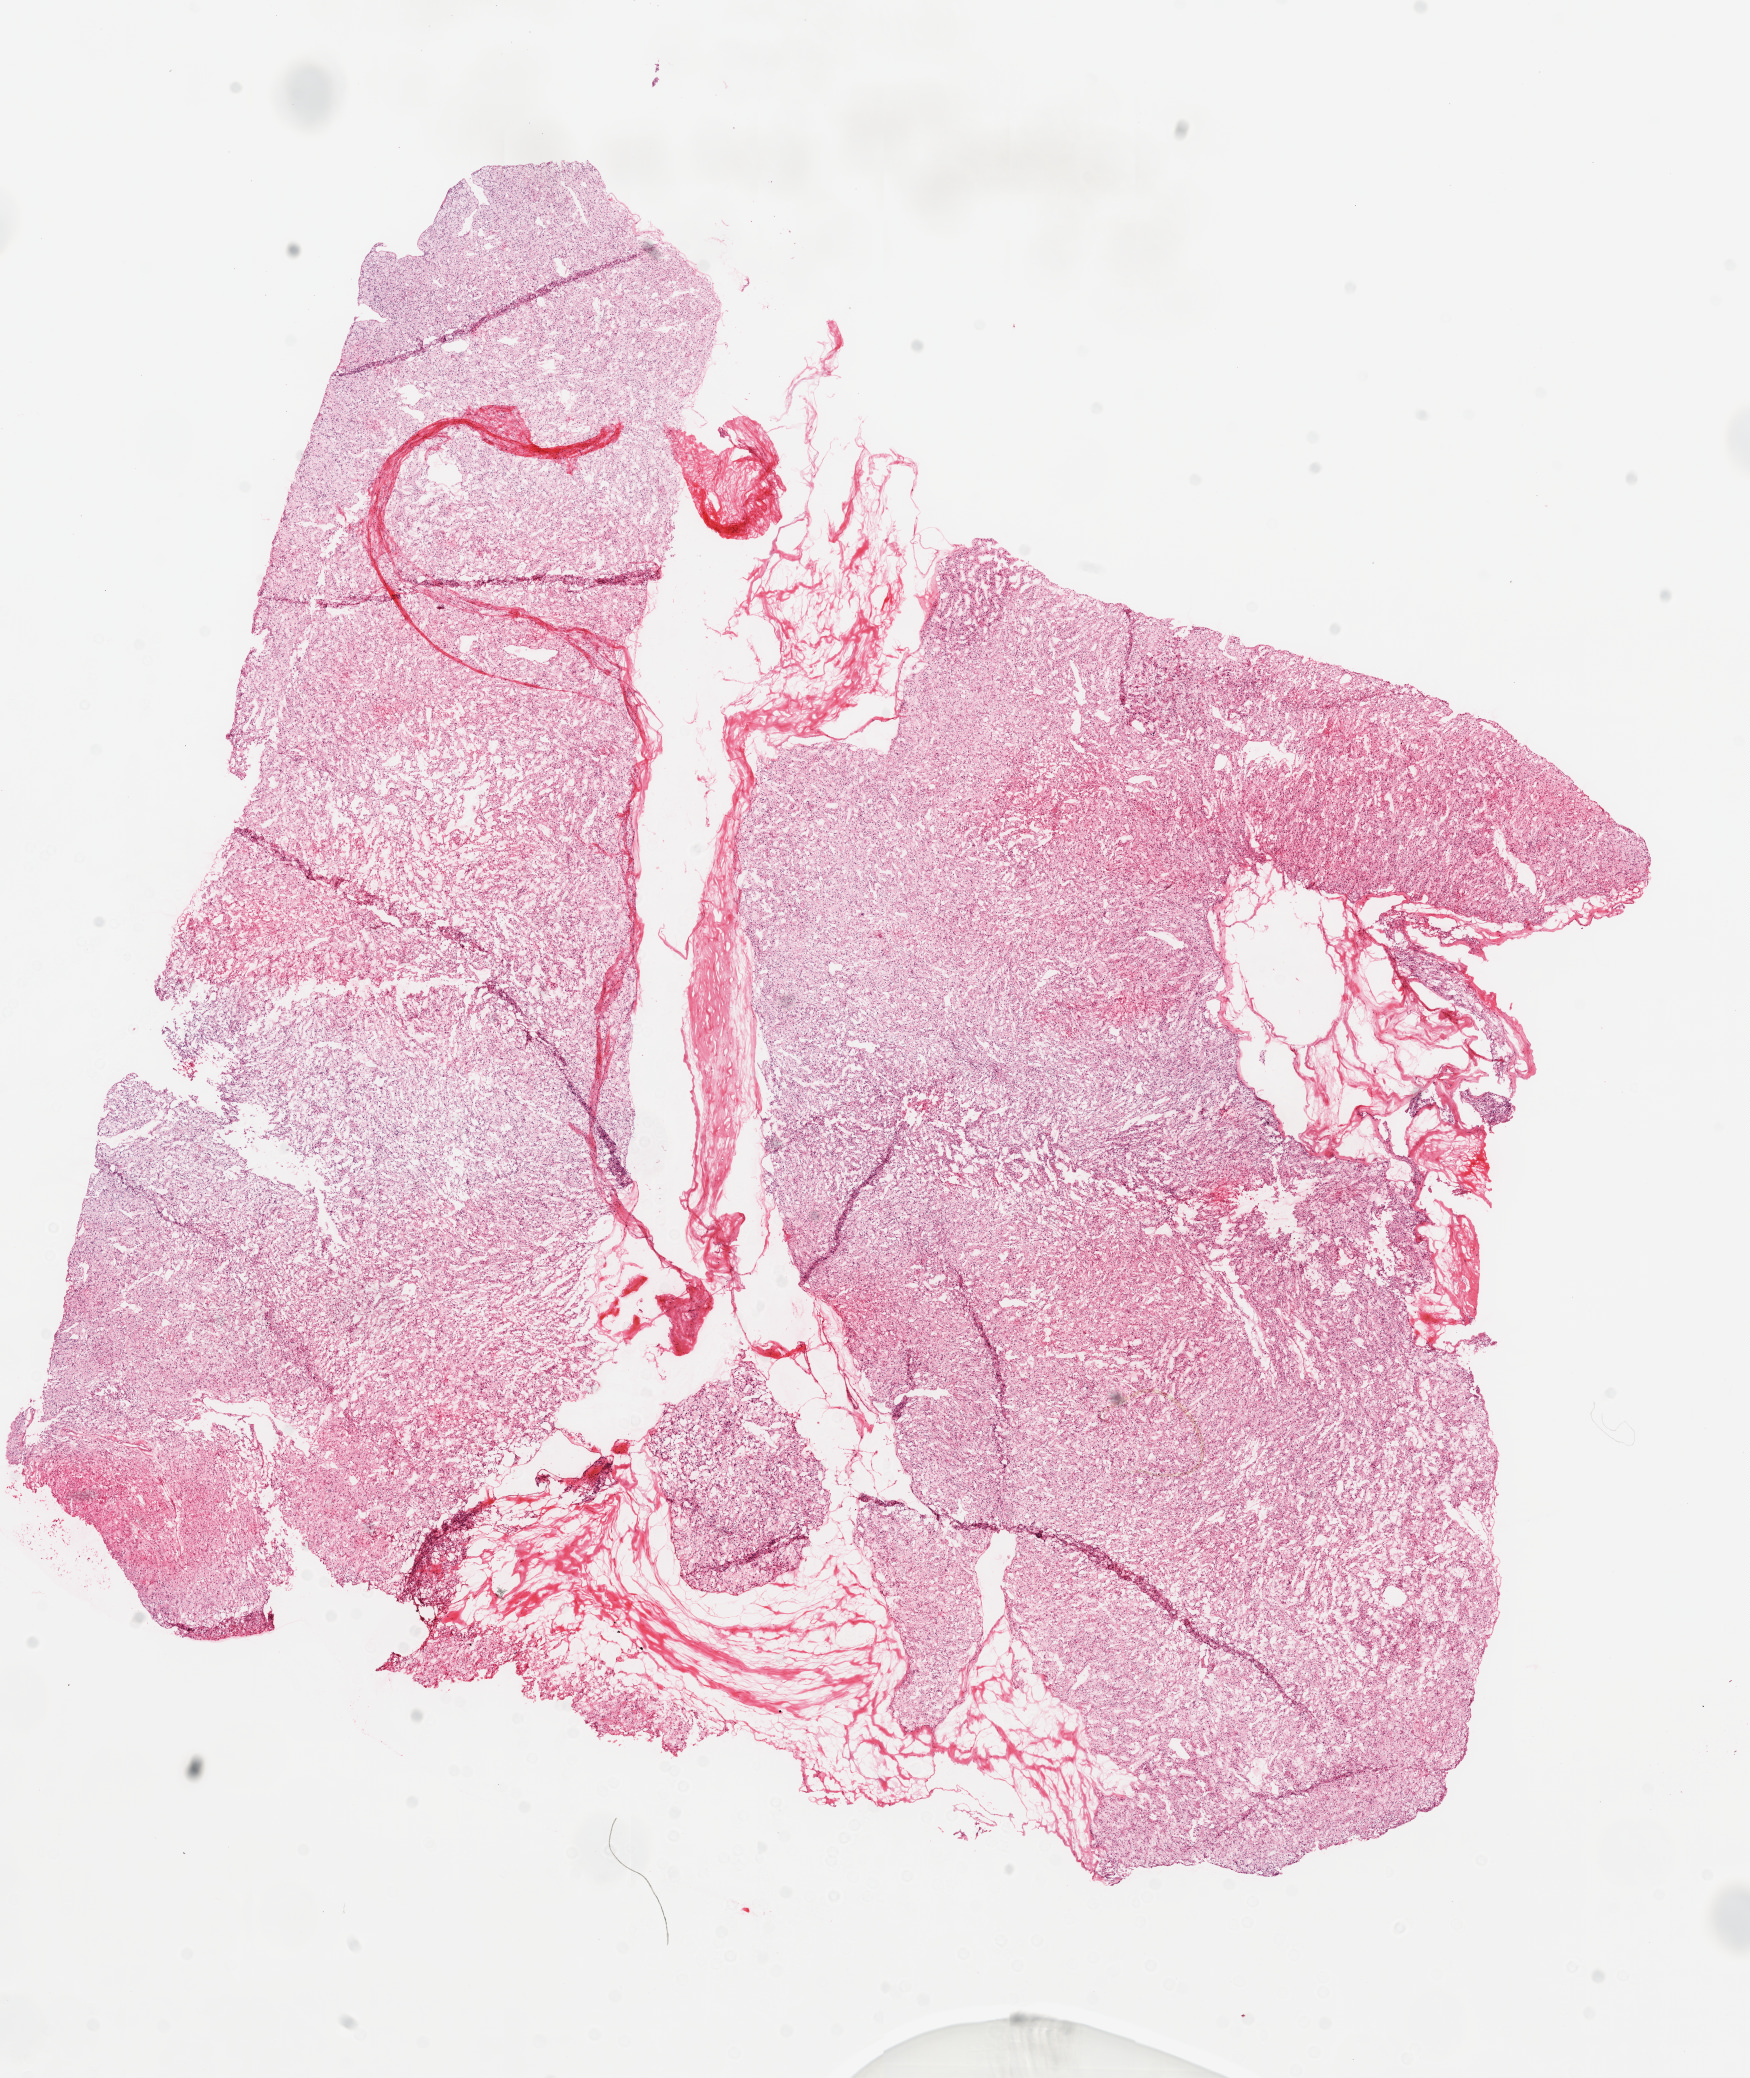
Whole-slide histology image, H&E-stained — a low-resolution overview of the entire scanned area, about 14.0 x 16.7 mm; frozen section; sample: primary tumour, kidney. Male, age 74 years at initial diagnosis. Histologic grade: G3 (poorly differentiated). Pathologist review of this section (percent, as recorded): tumour cells 90%, tumour nuclei 85%, normal cells 0%, stromal cells 10%, necrosis 0%. Inflammatory infiltration, as recorded: lymphocyte infiltration 2%, monocyte infiltration 0%, neutrophil infiltration 0%.
• histologic diagnosis: Clear cell adenocarcinoma, NOS
• laterality: left
• TNM: T2 N0 M0
• AJCC pathologic stage: II (6th edition)
• lymph nodes positive (case pathology): 0 of 13 examined